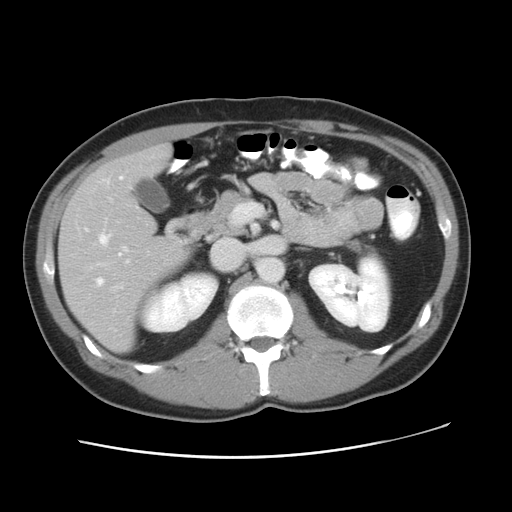
Contrast-enhanced abdominal CT, one axial slice. Position 25 of 49 along the scan axis. 120 kVp. Intravenous contrast given. Soft-tissue window (W 400 / L 40 HU). 5 mm slice thickness. 512 × 512 image matrix, field of view 363 × 363 mm. Male patient, age 41 years. Case-level facts recorded for this patient, not image findings: diagnosis: colorectal cancer liver metastases, imaged before liver resection; multiple liver metastases: yes; largest metastasis: 0.7 cm; disease in both lobes: yes.
Structures marked on this image (expert manual segmentation):
- hepatic veins: bounding box <94,175,238,287> (left, top, right, bottom; pixels)
- liver: <59,147,184,351>
- planned liver remnant (the part of the liver to remain after resection): <110,146,171,185>
- portal vein (with intrahepatic branches): <111,286,120,290>